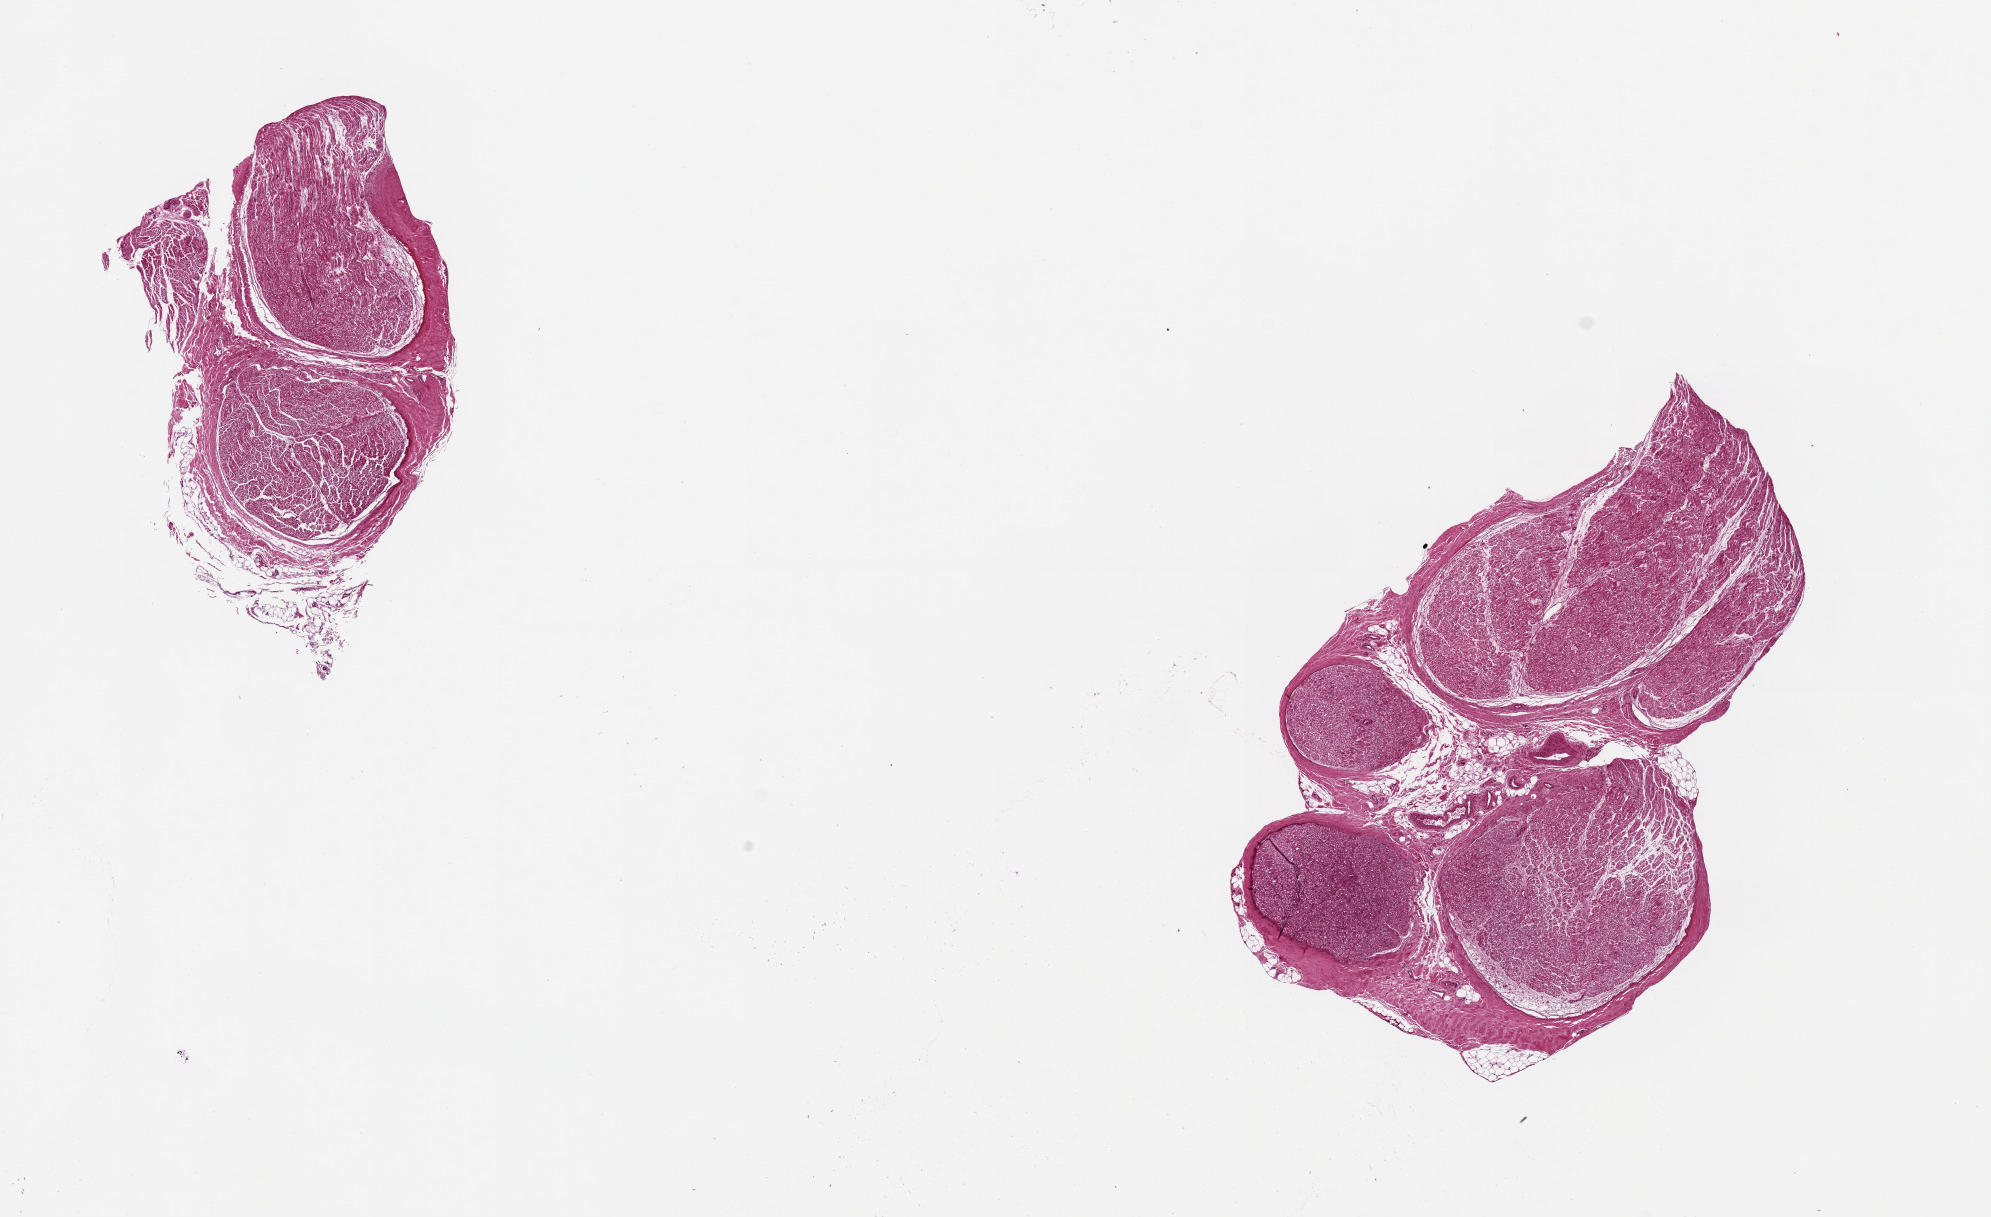
Digitized H&E-stained section, whole scanned area (about 15.8 x 9.6 mm, from a 20x scan) shown as a low-resolution overview, PAXgene-fixed paraffin-embedded (PFPE) section, sampled site (target tissue): tibial nerve, tissue donor sample. Donor: male.
Review note (as recorded): 2 pieces ~4mm d. Good clean specimens.